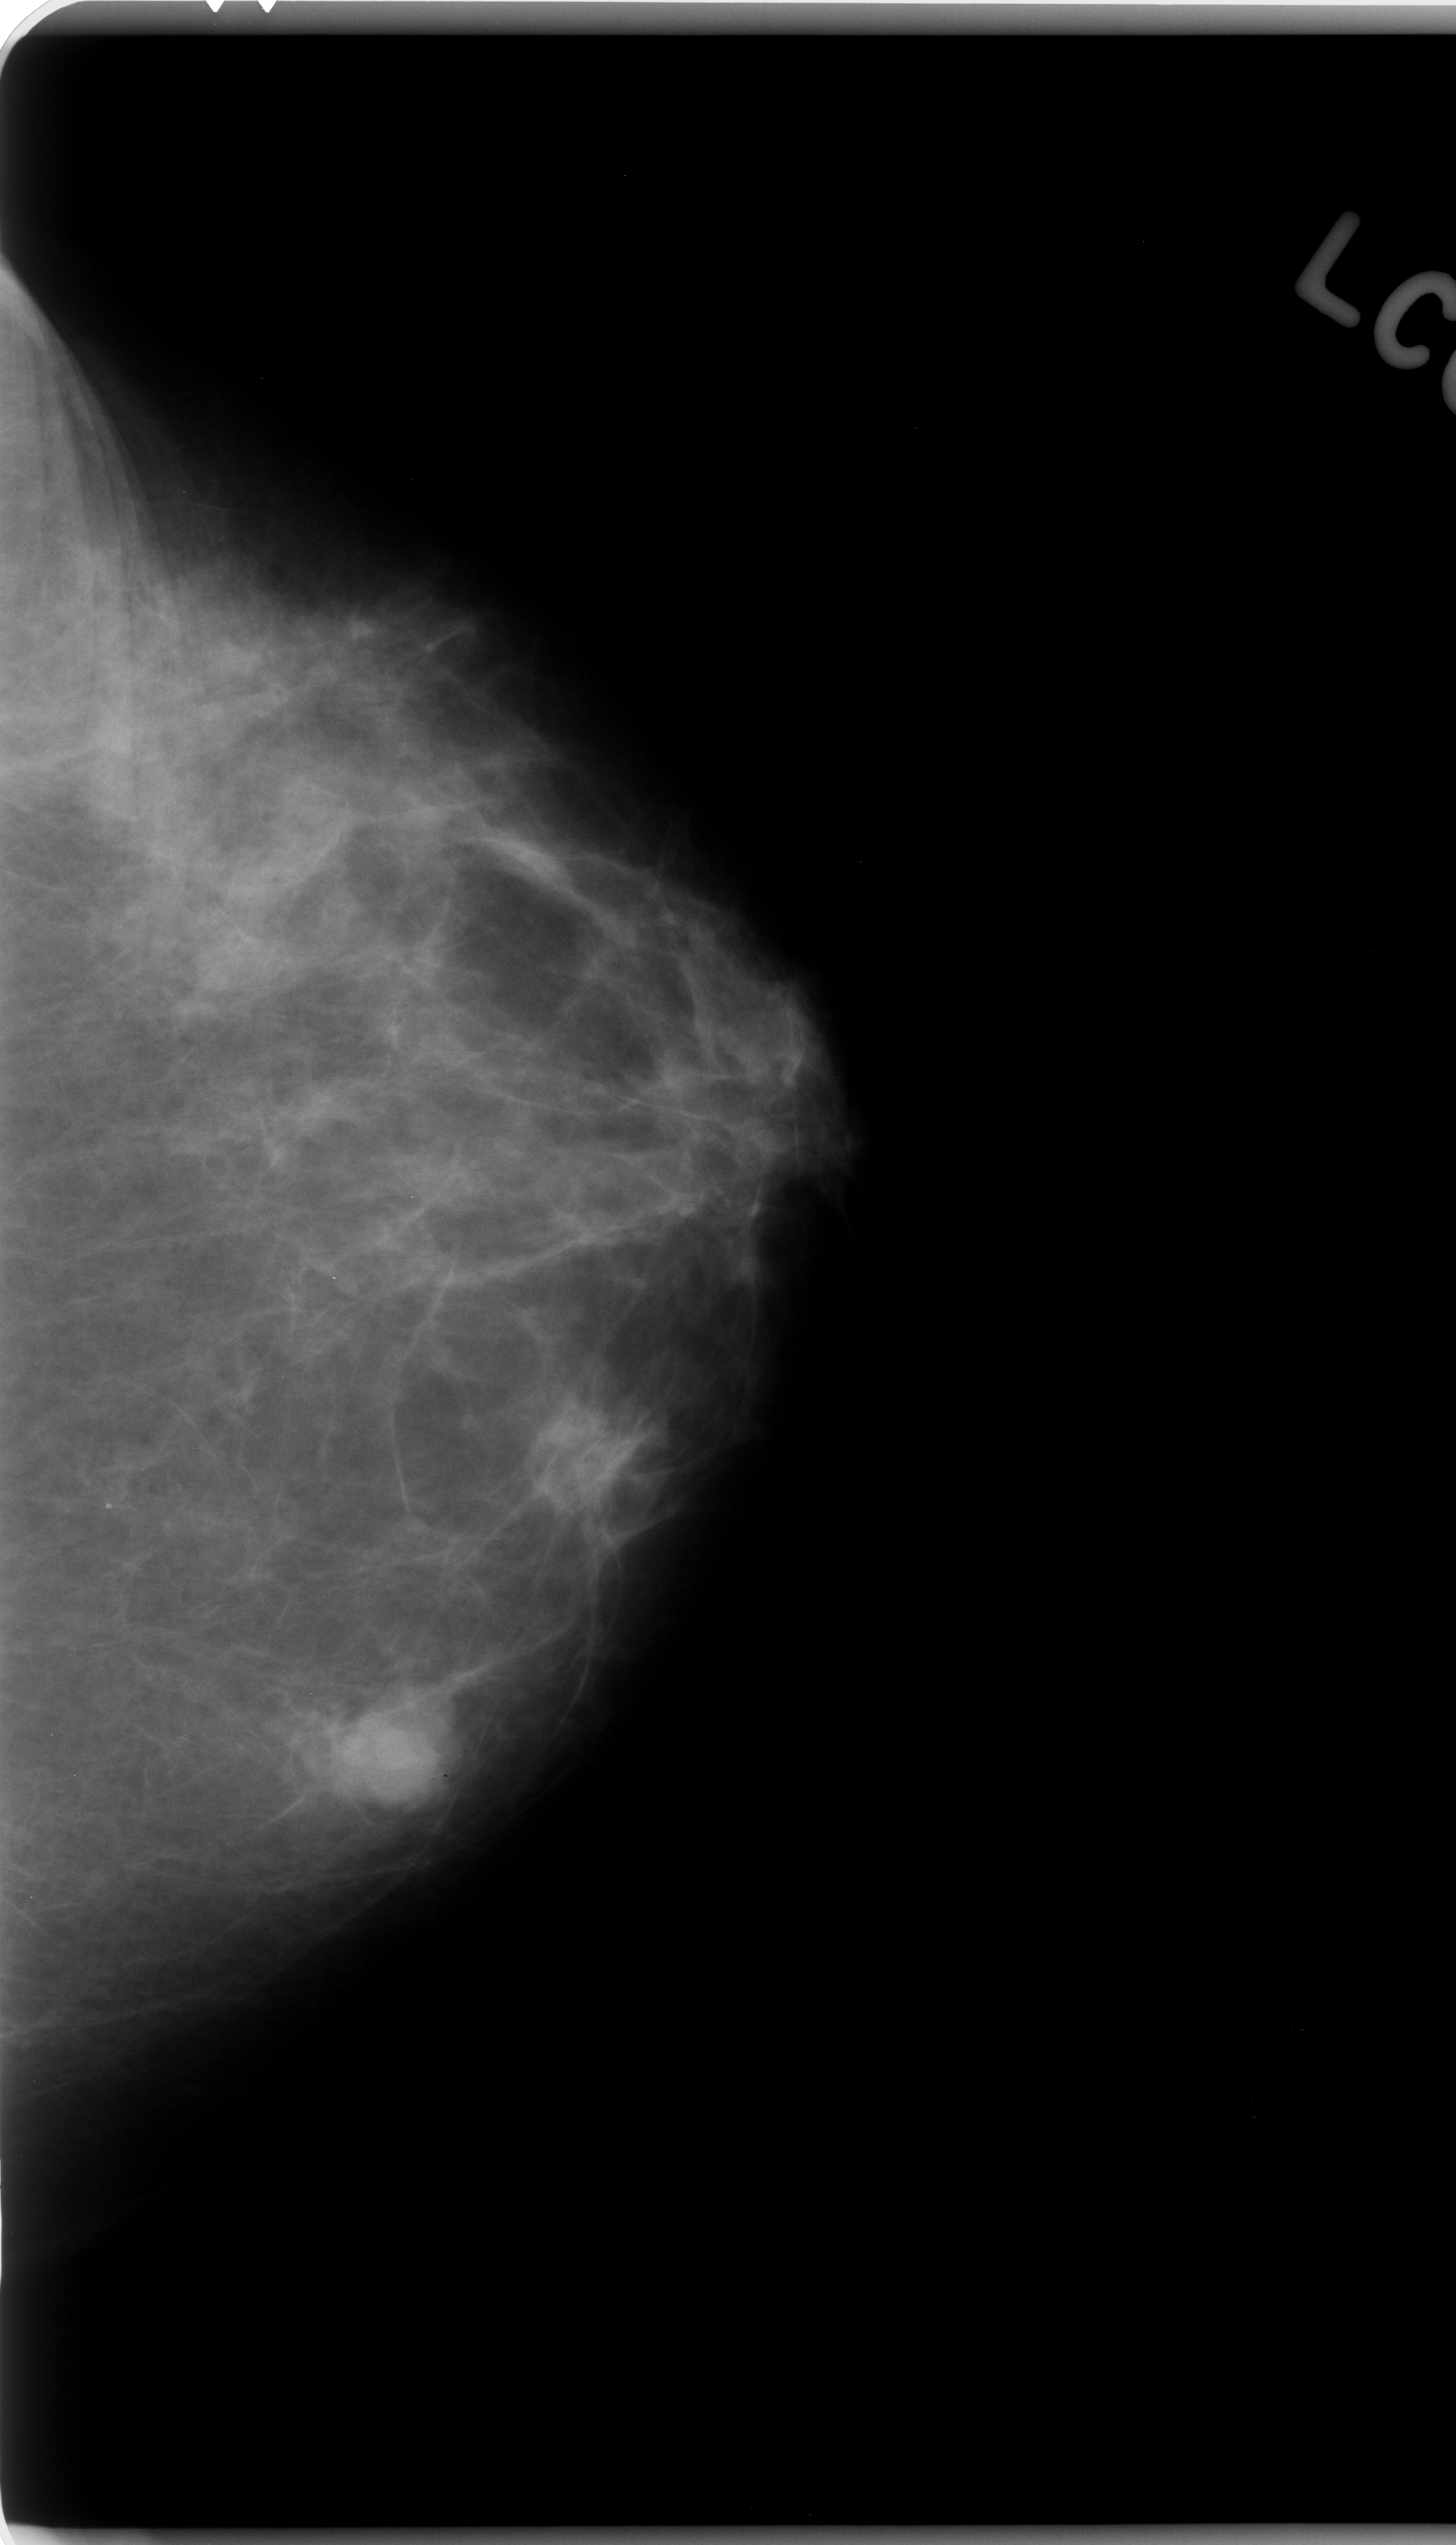
Digitized screen-film mammogram. Left breast. Craniocaudal (CC) view. BI-RADS breast density category 2 (scale 1–4). 1456 × 2545 image matrix.
Marked abnormalities (boxes around the expert regions of interest):
- mass, shape lobulated, margins microlobulated; BI-RADS assessment category 5; subtlety rating 5 on a 1 (subtle) to 5 (obvious) scale; pathology (as recorded): malignant: bounding box (x1, y1, x2, y2) in pixels: (302, 1678, 462, 1818)